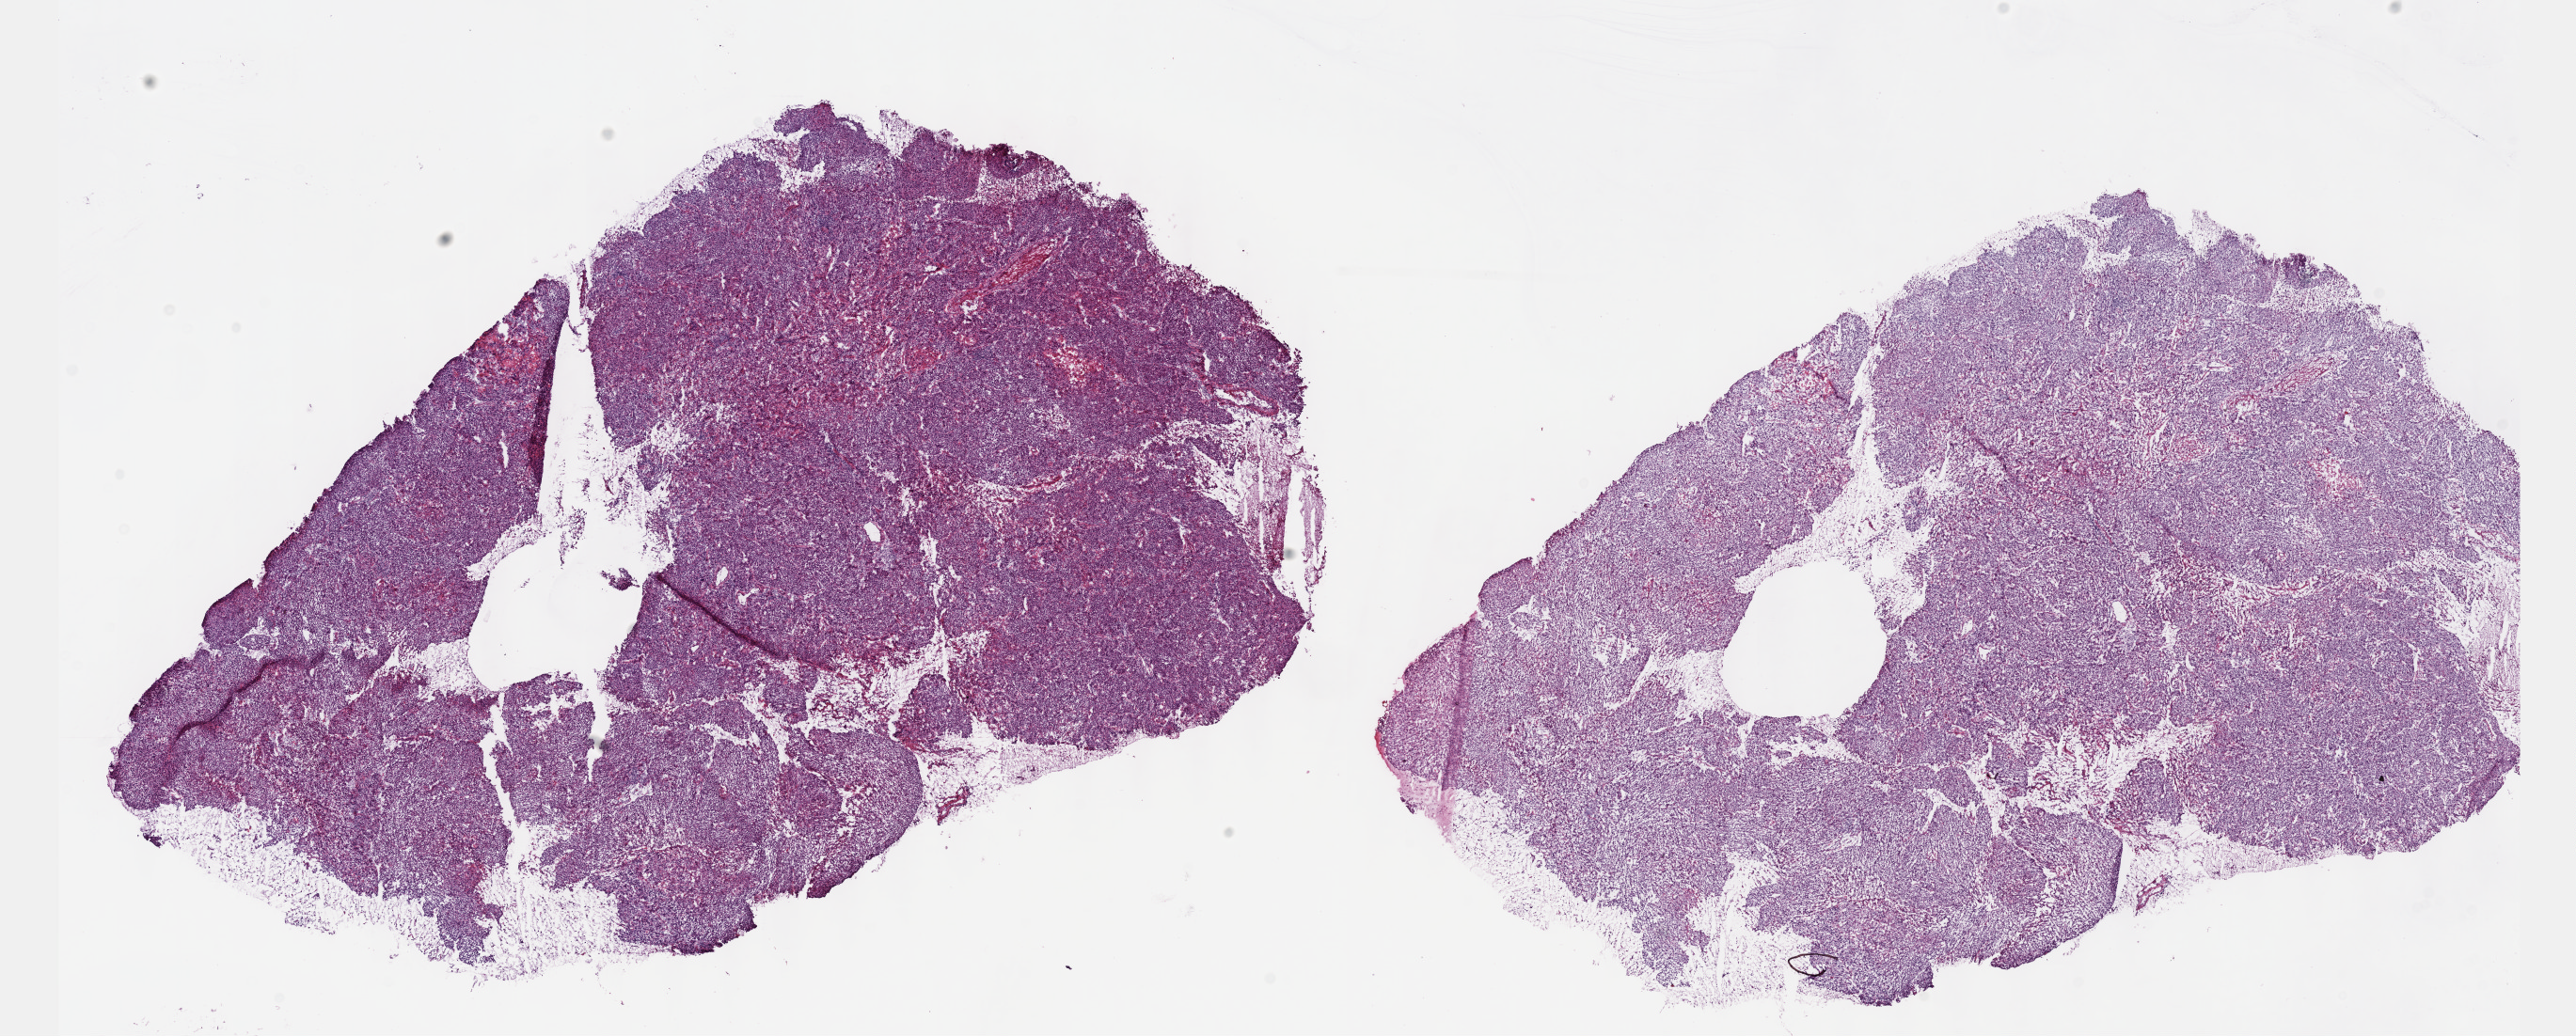
Digitized H&E-stained tissue section (whole slide), shown as a low-resolution overview of the whole scanned area (about 22.1 x 8.9 mm). Frozen section from the top of the tissue portion. Cervix, primary tumour sample. Female patient; age at initial diagnosis 29 years. Histologic grade: G2 (moderately differentiated). Pathologist review of this section (percent, as recorded): tumour cells 100%, tumour nuclei 80%, normal cells 0%, stromal cells 0%, necrosis 0%. Infiltration values recorded for this section: lymphocyte infiltration 2%, monocyte infiltration 0%, neutrophil infiltration 0%.
* FIGO stage: IVB
* histologic diagnosis: Squamous cell carcinoma, NOS (cervix uteri)